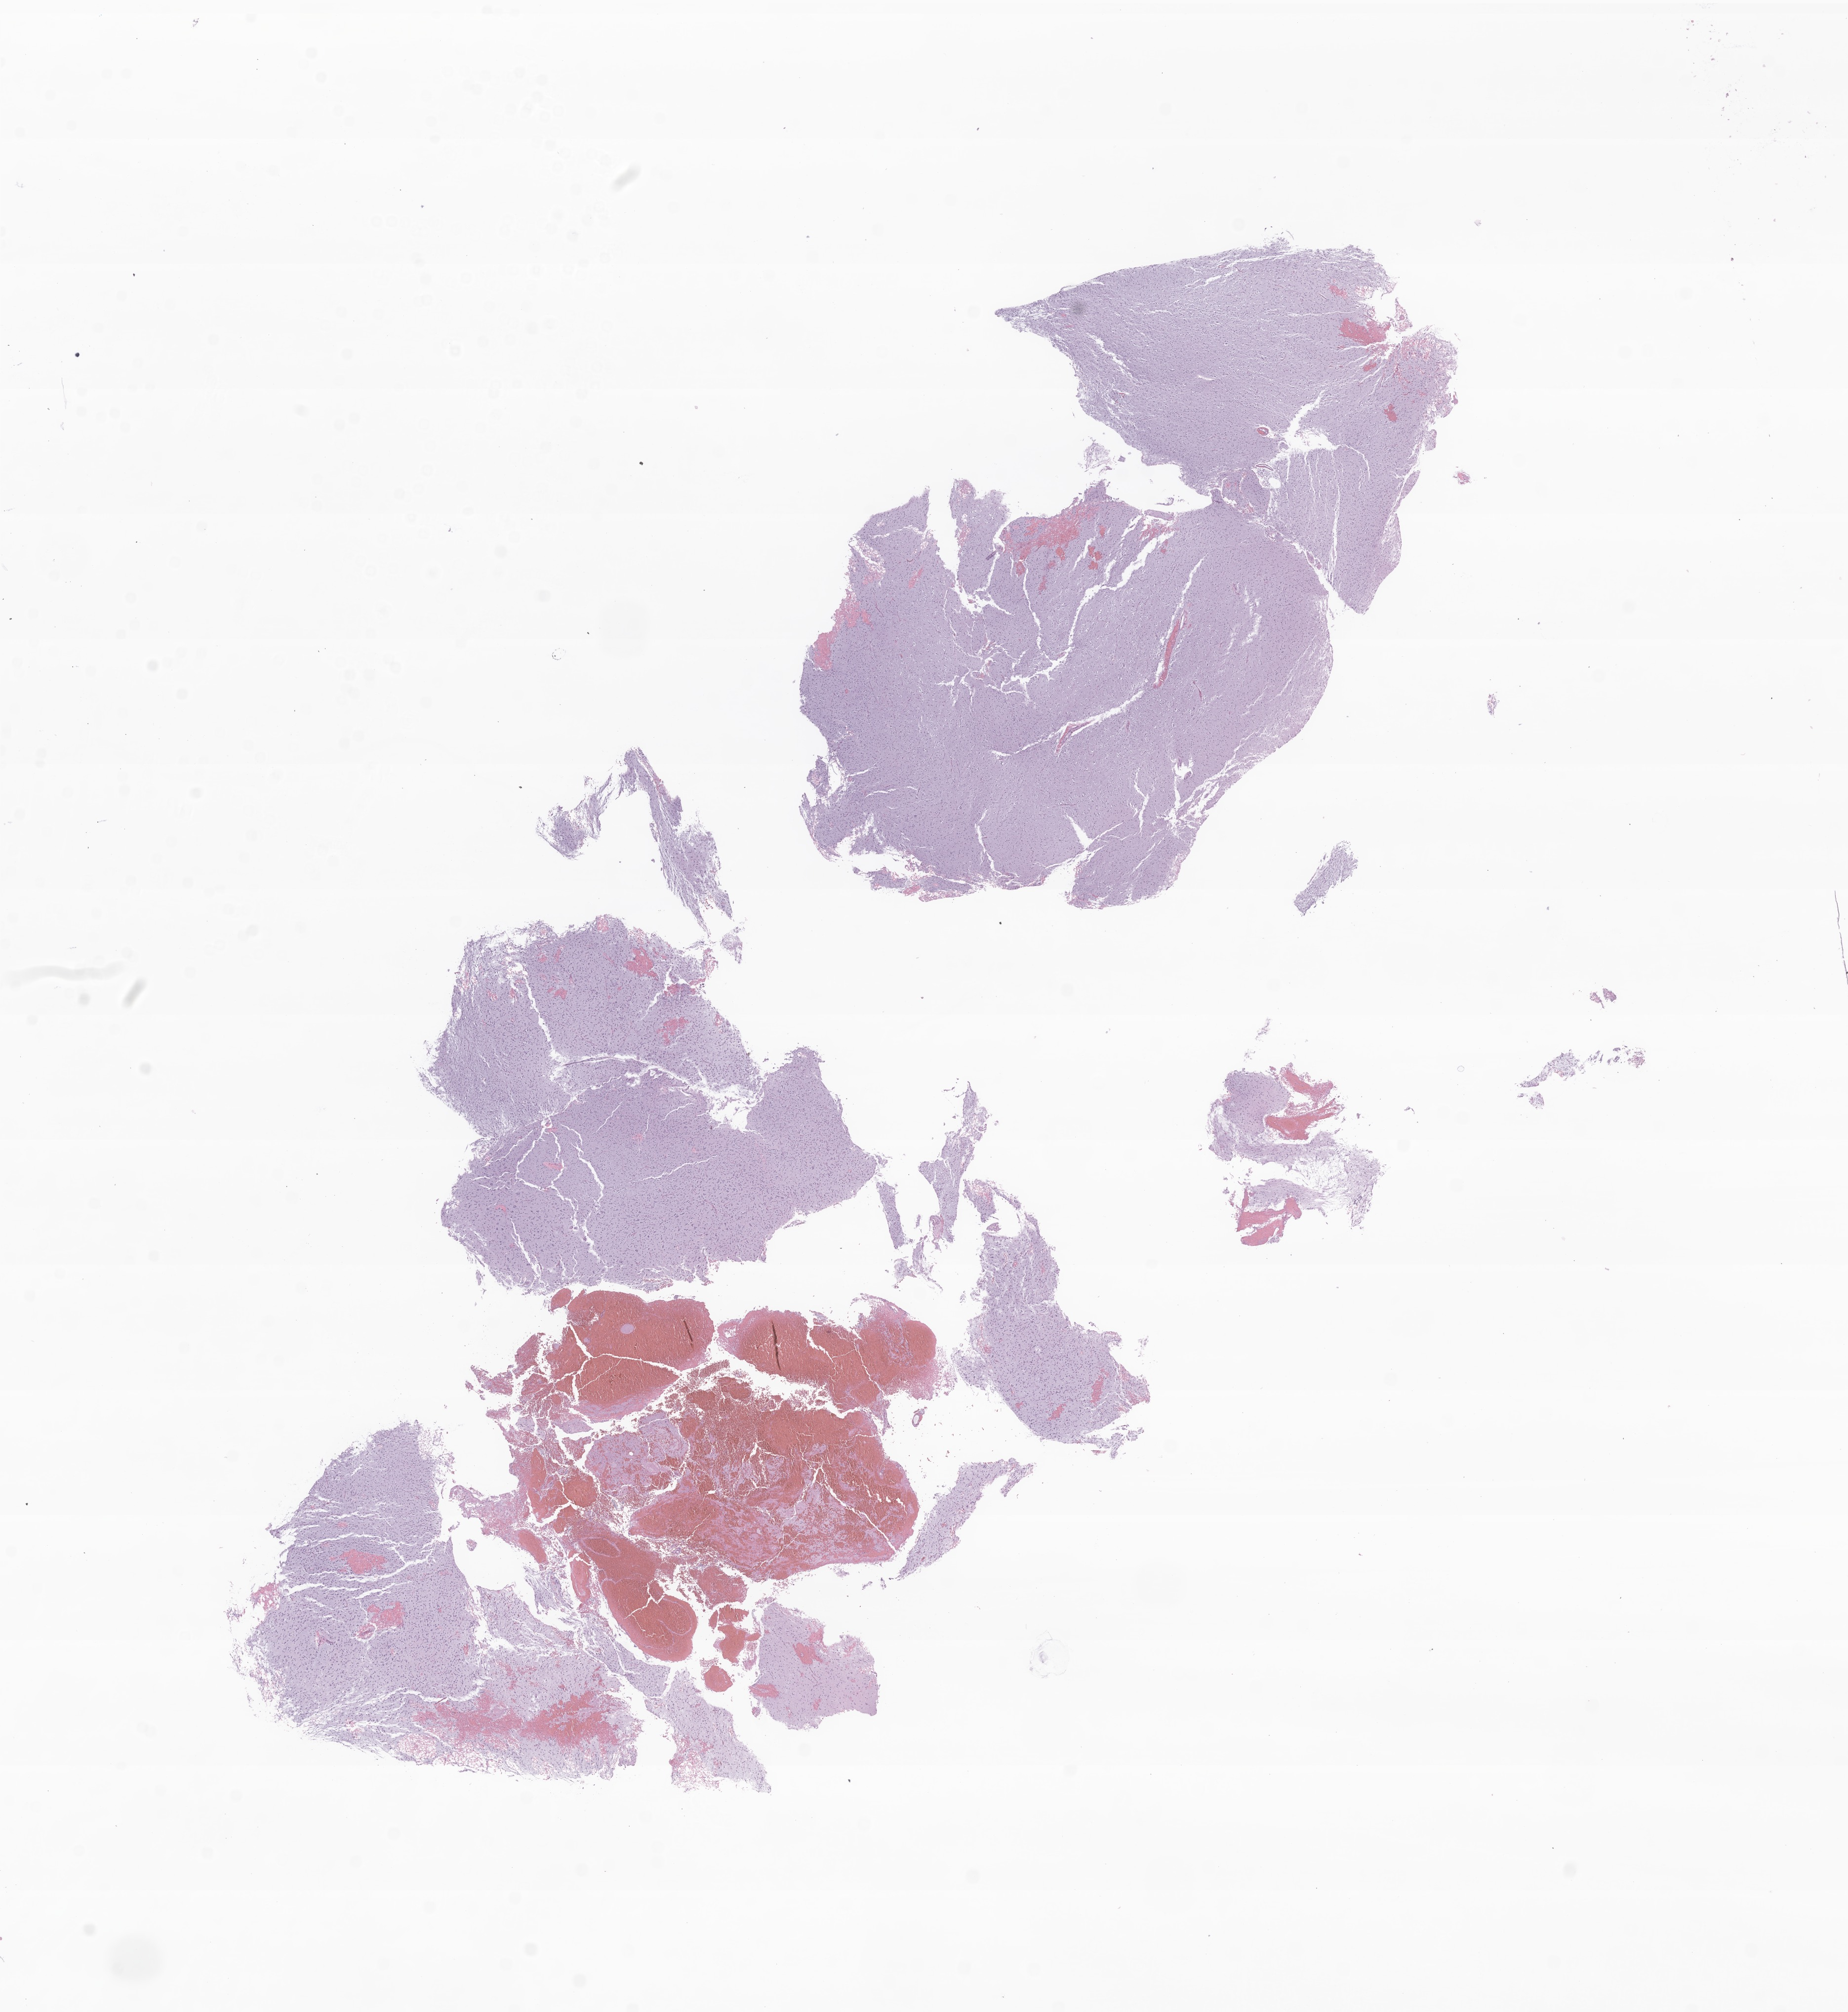
Digitized hematoxylin and eosin (H&E)-stained section of tumor tissue from the brain — a low-resolution overview of the entire scanned area, about 15.8 x 17.2 mm, FFPE section. Patient: female, age 38 months (3 years 2 months).
Diagnosis: Ganglioglioma, NOS.